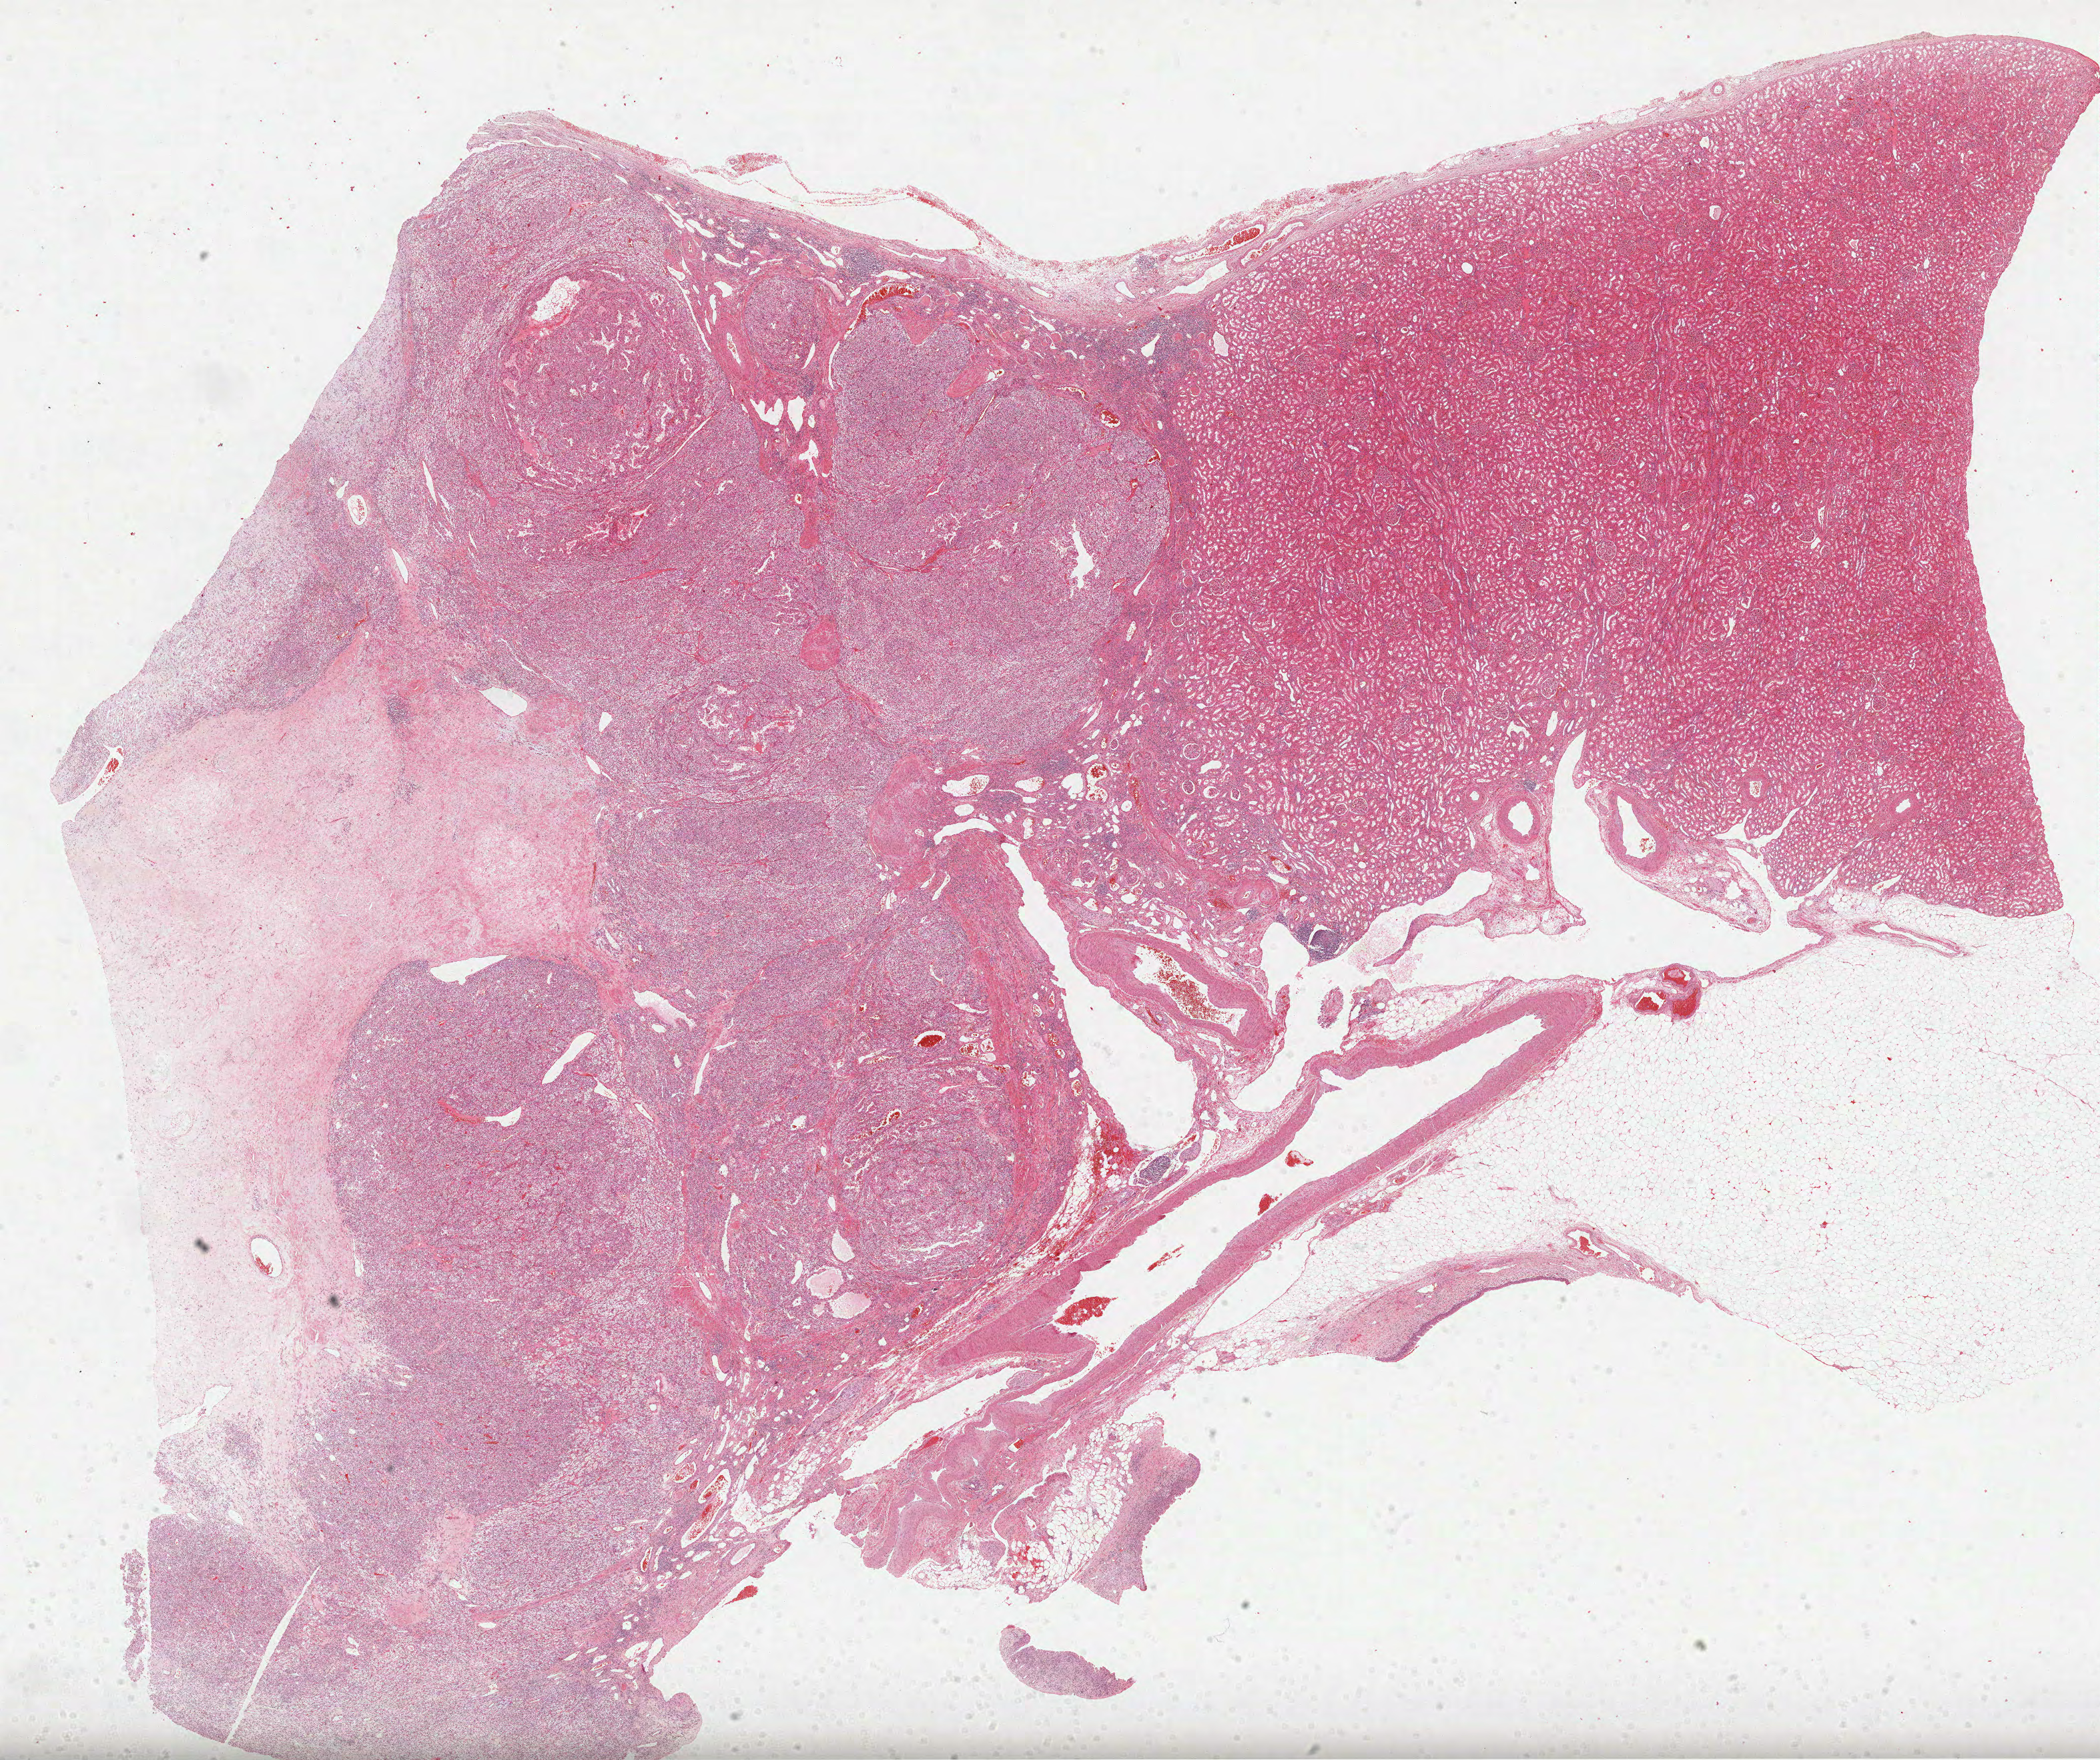
Digitized H&E tissue section (whole slide) — shown as a low-resolution overview of the whole scanned area (about 25.4 x 21.3 mm). Formalin-fixed paraffin-embedded (FFPE) diagnostic section. Sample: primary tumour, kidney. Female patient; age at initial diagnosis 62 years. Histologic grade: G3 (poorly differentiated).
AJCC pathologic stage: III (6th edition). Laterality: right. Histologic diagnosis: Clear cell adenocarcinoma, NOS.